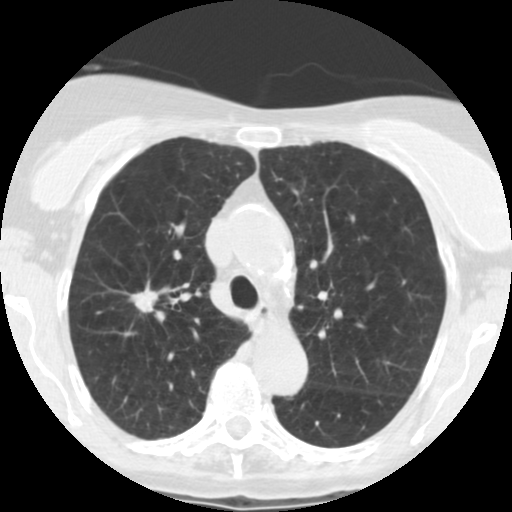
Axial slice from a low-dose chest CT screening exam. Baseline annual screen. Lung window (W 1500 / L -600 HU). 2.5 mm slice thickness. Standard (soft-tissue) reconstruction kernel (STANDARD). Slice 175 of 246 in the series. 512 × 512 image matrix. Female participant, aged 67 years at enrolment. Former smoker at enrolment.
Expert reader's lesion annotation, bounding box <114,280,172,322> (left, top, right, bottom; pixels). The screening reader recorded 6 non-calcified nodules or masses ≥4 mm on this exam (right upper lobe, right middle lobe, left lower lobe, right middle lobe, left lower lobe, left lower lobe); which of them this box marks is not recorded. Lung cancer was diagnosed 15 days after this screen: adenocarcinoma, NOS, right upper lobe, moderately differentiated (G2), stage IA (AJCC 6th edition), 14 mm at pathology.